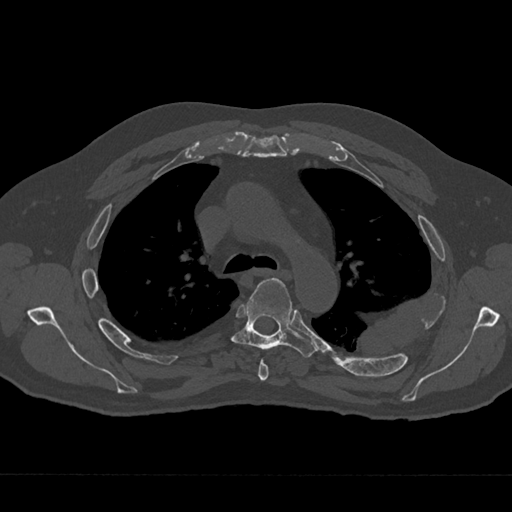
CT including the spine, one axial slice; position 483 of 797 along the scan axis; reconstruction kernel Br40s/3; bone window (W 1800 / L 400 HU); 512 × 512 image matrix, field of view 377 × 377 mm. Male patient, age 75 years. Case-level facts recorded for this patient, not image findings: primary cancer: renal.
Structures marked on this image (semi-automatic segmentation, software-assisted and operator-edited):
- T4 vertebra: bounding box <258,359,269,381> (left, top, right, bottom; pixels)
- T5 vertebra: <230,278,316,358>